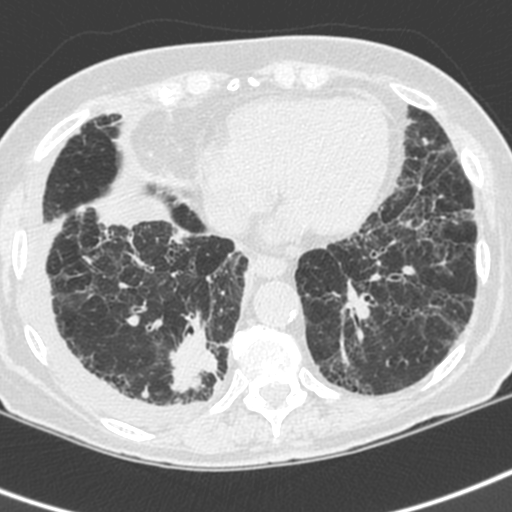
Low-dose screening chest CT, axial slice. First (baseline) screen. Lung window (W 1500 / L -600 HU). 1.3 mm slice thickness. 120 kVp. 512 × 512 image matrix. Female, age 73 years at enrolment. Current smoker at enrolment.
Expert-annotated lung lesion, bounding box [x1, y1, x2, y2] px = [155, 316, 235, 406]. The exam's reader record, not a measurement of the box and not confirmed to be the same lesion: non-calcified nodule or mass ≥4 mm, right lower lobe, 35 × 30 mm, spiculated (stellate) margins, soft tissue attenuation. Official screen result: positive, change unspecified: nodule(s) >= 4 mm or enlarging nodule(s), mass(es), or other non-specific abnormalities suspicious for lung cancer. Later outcome: lung cancer diagnosed 22 days after this screen — adenocarcinoma, NOS, right lower lobe, stage IV (AJCC 6th edition), 35 mm at pathology.